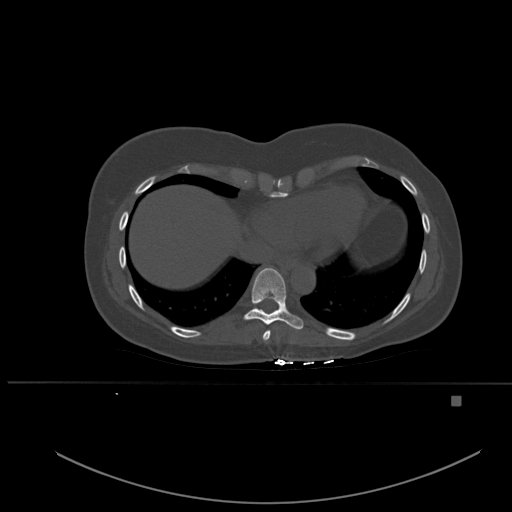
CT including the spine, one axial slice. Position 306 of 651 along the scan axis. Bone window (W 1800 / L 400 HU). 1.5 mm slice thickness. 512 × 512 image matrix. Patient: female, 49 years. From the clinical record (not read from this slice): primary cancer: breast; vertebrae with lytic lesions (as recorded): L3, T12, L4.
Annotated regions visible in this slice (semi-automatically segmented with operator editing):
- T8 vertebra: bounding box (x1, y1, x2, y2) in pixels: (262, 331, 270, 341)
- T9 vertebra: (244, 268, 304, 334)